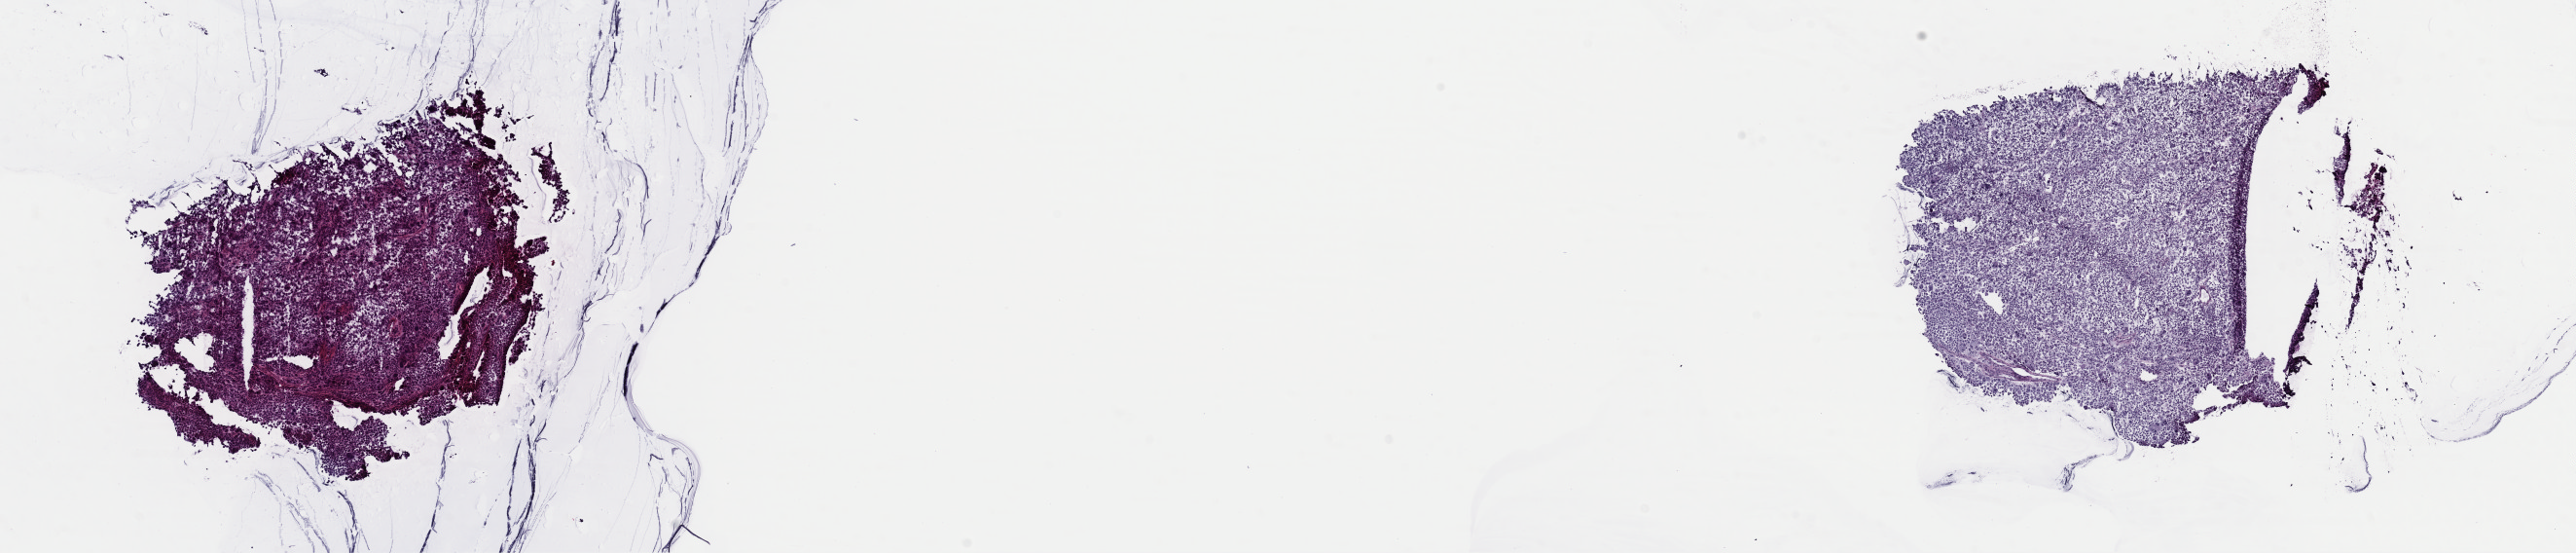
Whole-slide histology image, Hematoxylin and eosin (H&E) stained, whole scanned area (about 20.9 x 4.5 mm) shown as a low-resolution overview; frozen section; sample: primary tumour, skin. Male, age 71 years at initial diagnosis. Pathologist review of this section (percent, as recorded): tumour cells 85%, tumour nuclei 85%, normal cells 0%, stromal cells 15%, necrosis 0%. Infiltration values recorded for this section: lymphocyte infiltration 2%, monocyte infiltration 0%, neutrophil infiltration 1%.
Diagnosis: Malignant melanoma, NOS.